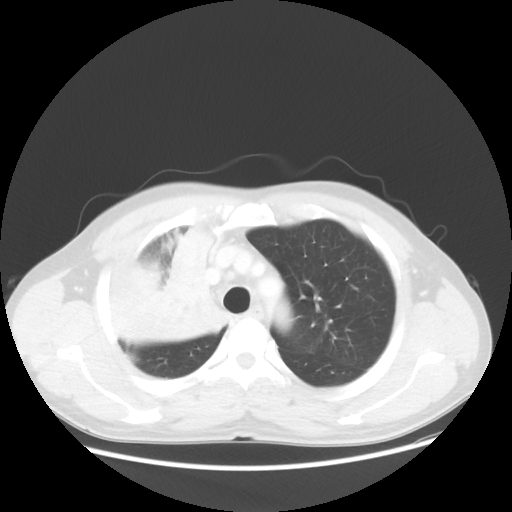
Chest CT, one axial slice. Position 42 of 56 along the scan axis. 100 kVp. Lung window (W 1500 / L -600 HU). 5 mm slice thickness. 512 × 512 image matrix, field of view 398 × 398 mm. Male patient, age 60 years. Case-level facts recorded for this patient, not image findings: clinical TNM (as recorded): T2a N1 M0.
Structures marked on this image (bounding box drawn by a radiologist):
- lung tumour (recorded histology: squamous cell carcinoma): bounding box <124,209,237,355> (left, top, right, bottom; pixels)